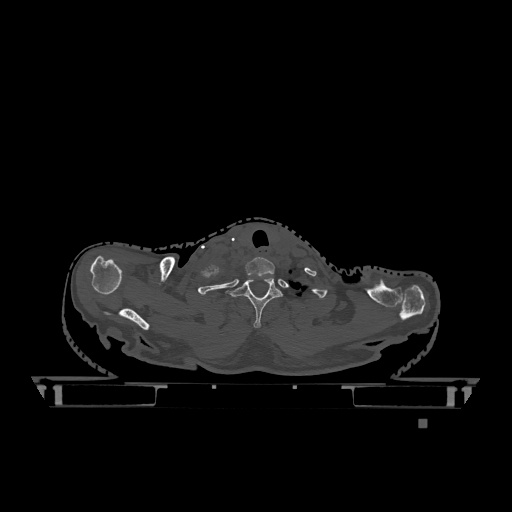
CT including the spine, one axial slice. Position 1002 of 1317 along the scan axis. Bone window (W 1800 / L 400 HU). 512 × 512 image matrix, field of view 500 × 500 mm. Female patient, age 74 years. From the clinical record (not read from this slice): primary cancer: lung; vertebrae with lytic lesions (as recorded): T1, T4, T5, T6, L4, L5.
Structures marked on this image (semi-automatic segmentation, software-assisted and operator-edited):
- T1 vertebra: box from (x=230, y=276) to (x=283, y=328) px